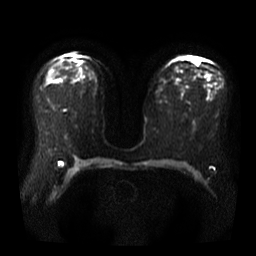
Breast MRI, one axial slice. Slice 23 of 40 in the series (ordered by position). Diffusion-weighted series; image 2 of 4 stored at this slice position (different b-values; order by instance number). 3 T. 5 mm slice thickness. 256 × 256 image matrix, field of view 360 × 360 mm. Female patient.
Outlined on this slice (outlined manually by an expert reader):
- tumour on diffusion-weighted imaging: box from (x=195, y=56) to (x=201, y=61) px